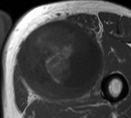
MRI of an extremity soft-tissue mass, one axial slice. Position 41 of 55 along the scan axis. MR volume resampled by the dataset authors to the PET/CT grid (not the native acquisition matrix). 3.27 mm slice thickness. 131 × 118 image matrix, field of view 128 × 115 mm. Male patient. From the clinical record (not read from this slice): histological type: pleiomorphic liposarcoma; grade: high; site of the primary tumour: left thigh.
Outlined on this slice (expert contour drawn on MRI and transferred to this co-registered scan by the dataset authors):
- gross tumour volume including surrounding oedema: bounding box (x1, y1, x2, y2) in pixels: (18, 18, 104, 95)
- gross tumour volume (mass): (18, 20, 101, 95)